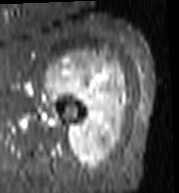
MRI of an extremity soft-tissue mass, one axial slice; position 79 of 103 along the scan axis; STIR; MR volume resampled by the dataset authors to the PET/CT grid (not the native acquisition matrix); 3.27 mm slice thickness; 179 × 193 image matrix, field of view 175 × 188 mm. Female patient. Case-level facts recorded for this patient, not image findings: histological type: undifferentiated – high grade; grade: high; site of the primary tumour: left thigh.
Outlined on this slice (expert contour drawn on MRI and transferred to this co-registered scan by the dataset authors):
- gross tumour volume including surrounding oedema: bounding box [x1, y1, x2, y2] px = [43, 51, 128, 170]
- gross tumour volume (mass): [45, 53, 128, 170]